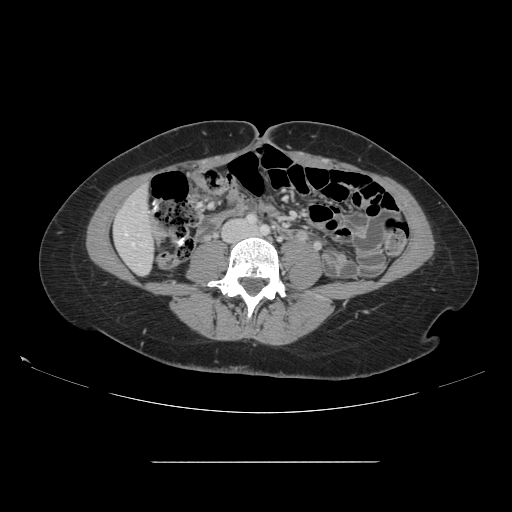
Contrast-enhanced abdominal CT, one axial slice; position 24 of 151 along the scan axis; 120 kVp; intravenous contrast given; soft-tissue window (W 400 / L 40 HU); 512 × 512 image matrix, field of view 421 × 421 mm. Female patient, age 46 years. Case-level facts recorded for this patient, not image findings: diagnosis: colorectal cancer liver metastases, imaged before liver resection; multiple liver metastases: yes; largest metastasis: 3 cm.
Annotated regions visible in this slice (expert manual segmentation):
- liver: bounding box <115,189,154,274> (left, top, right, bottom; pixels)
- planned liver remnant (the part of the liver to remain after resection): <115,189,154,274>